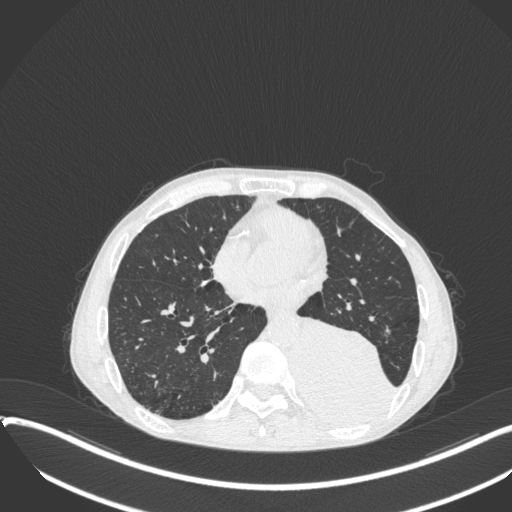
Chest CT, one axial slice; slice 140 of 400 in the series (ordered by position); reconstruction kernel B31f; lung window (W 1500 / L -600 HU); 512 × 512 image matrix. Patient: male, 57 years. From the clinical record (not read from this slice): clinical TNM (as recorded): T4 N0 M0.
Outlined on this slice (bounding box drawn by a radiologist):
- lung tumour (recorded histology: squamous cell carcinoma): bounding box [x1, y1, x2, y2] px = [290, 309, 396, 430]